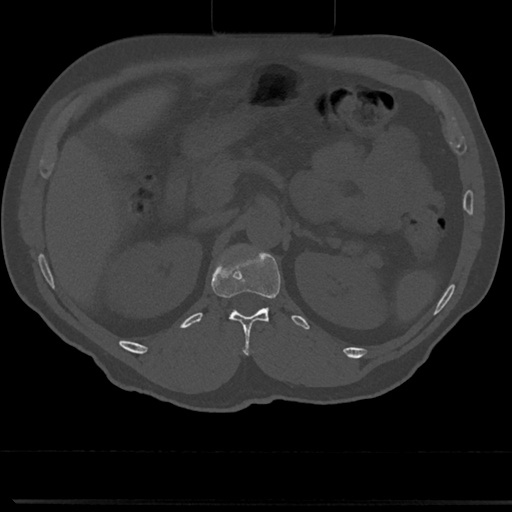
CT including the spine, one axial slice. Position 132 of 817 along the scan axis. 120 kVp. Bone window (W 1800 / L 400 HU). 0.5 mm slice thickness. 512 × 512 image matrix, field of view 355 × 355 mm. Male patient, age 61 years. Case-level facts recorded for this patient, not image findings: primary cancer: prostate.
Structures marked on this image (semi-automatic segmentation, software-assisted and operator-edited):
- T12 vertebra: bounding box <221,266,282,357> (left, top, right, bottom; pixels)